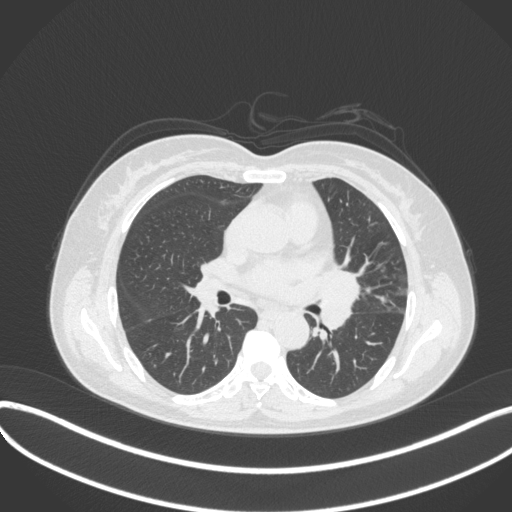
Chest CT, one axial slice. Reconstruction kernel B31f. 120 kVp. Lung window (W 1500 / L -600 HU). 1 mm slice thickness. 512 × 512 image matrix, field of view 400 × 400 mm. Female patient, age 54 years. Case-level facts recorded for this patient, not image findings: clinical TNM (as recorded): T2a N1 M0; histopathological grade: G3.
Annotated regions visible in this slice (rectangle marked by the reading radiologist):
- lung tumour (recorded histology: small cell carcinoma): box from (x=315, y=265) to (x=365, y=332) px